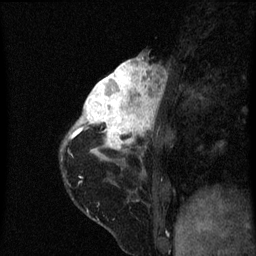
Breast MRI (dynamic contrast-enhanced), one sagittal slice. Slice 21 of 60 in the series (ordered by position). Dynamic contrast-enhanced series, image 2 of 3 at this slice position (ordered by acquisition). 1.5 T. TE 4.2 ms, TR 8 ms. 2 mm slice thickness. 256 × 256 image matrix, field of view 180 × 180 mm. Patient: female, 38 years.
Outlined on this slice (semi-automatically segmented with operator editing):
- analysis volume of interest (the breast-tissue region the enhancement analysis was run in; not a lesion): bounding box [x1, y1, x2, y2] px = [80, 60, 165, 151]
- tumour enhancement mask (voxels above the 70 % enhancement threshold inside the analysis volume of interest): [80, 60, 161, 149]